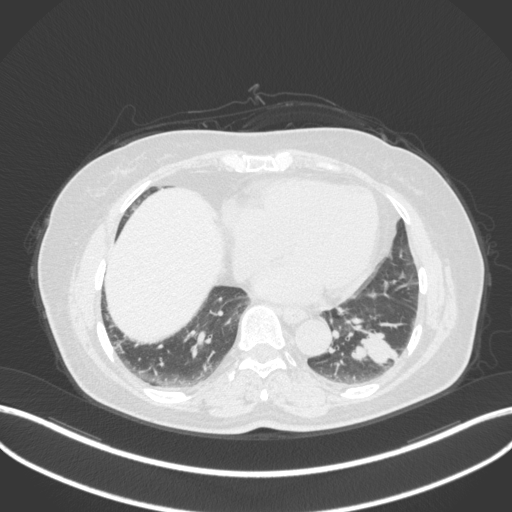
Chest CT, one axial slice. Slice 129 of 307 in the series (ordered by position). Reconstruction kernel B31f. Lung window (W 1500 / L -600 HU). 1 mm slice thickness. 512 × 512 image matrix, field of view 400 × 400 mm. Patient: female, 59 years. Case-level facts recorded for this patient, not image findings: clinical TNM (as recorded): T2a N0 M0; histopathological grade: G2-3.
Annotated regions visible in this slice (rectangle marked by the reading radiologist):
- lung tumour (recorded histology: adenocarcinoma): bounding box [x1, y1, x2, y2] px = [347, 321, 410, 371]